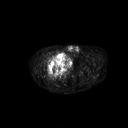
FDG PET of an extremity soft-tissue mass (from a PET/CT study), one axial slice; 3.27 mm slice thickness; 128 × 128 image matrix. Male patient, age 50 years. Case-level facts recorded for this patient, not image findings: histological type: undifferentiated - pleiomorphic; grade: high; site of the primary tumour: right thigh.
Structures marked on this image (expert contour drawn on MRI and transferred to this co-registered scan by the dataset authors):
- gross tumour volume including surrounding oedema: bounding box <49,52,65,68> (left, top, right, bottom; pixels)
- gross tumour volume (mass): <49,52,65,68>